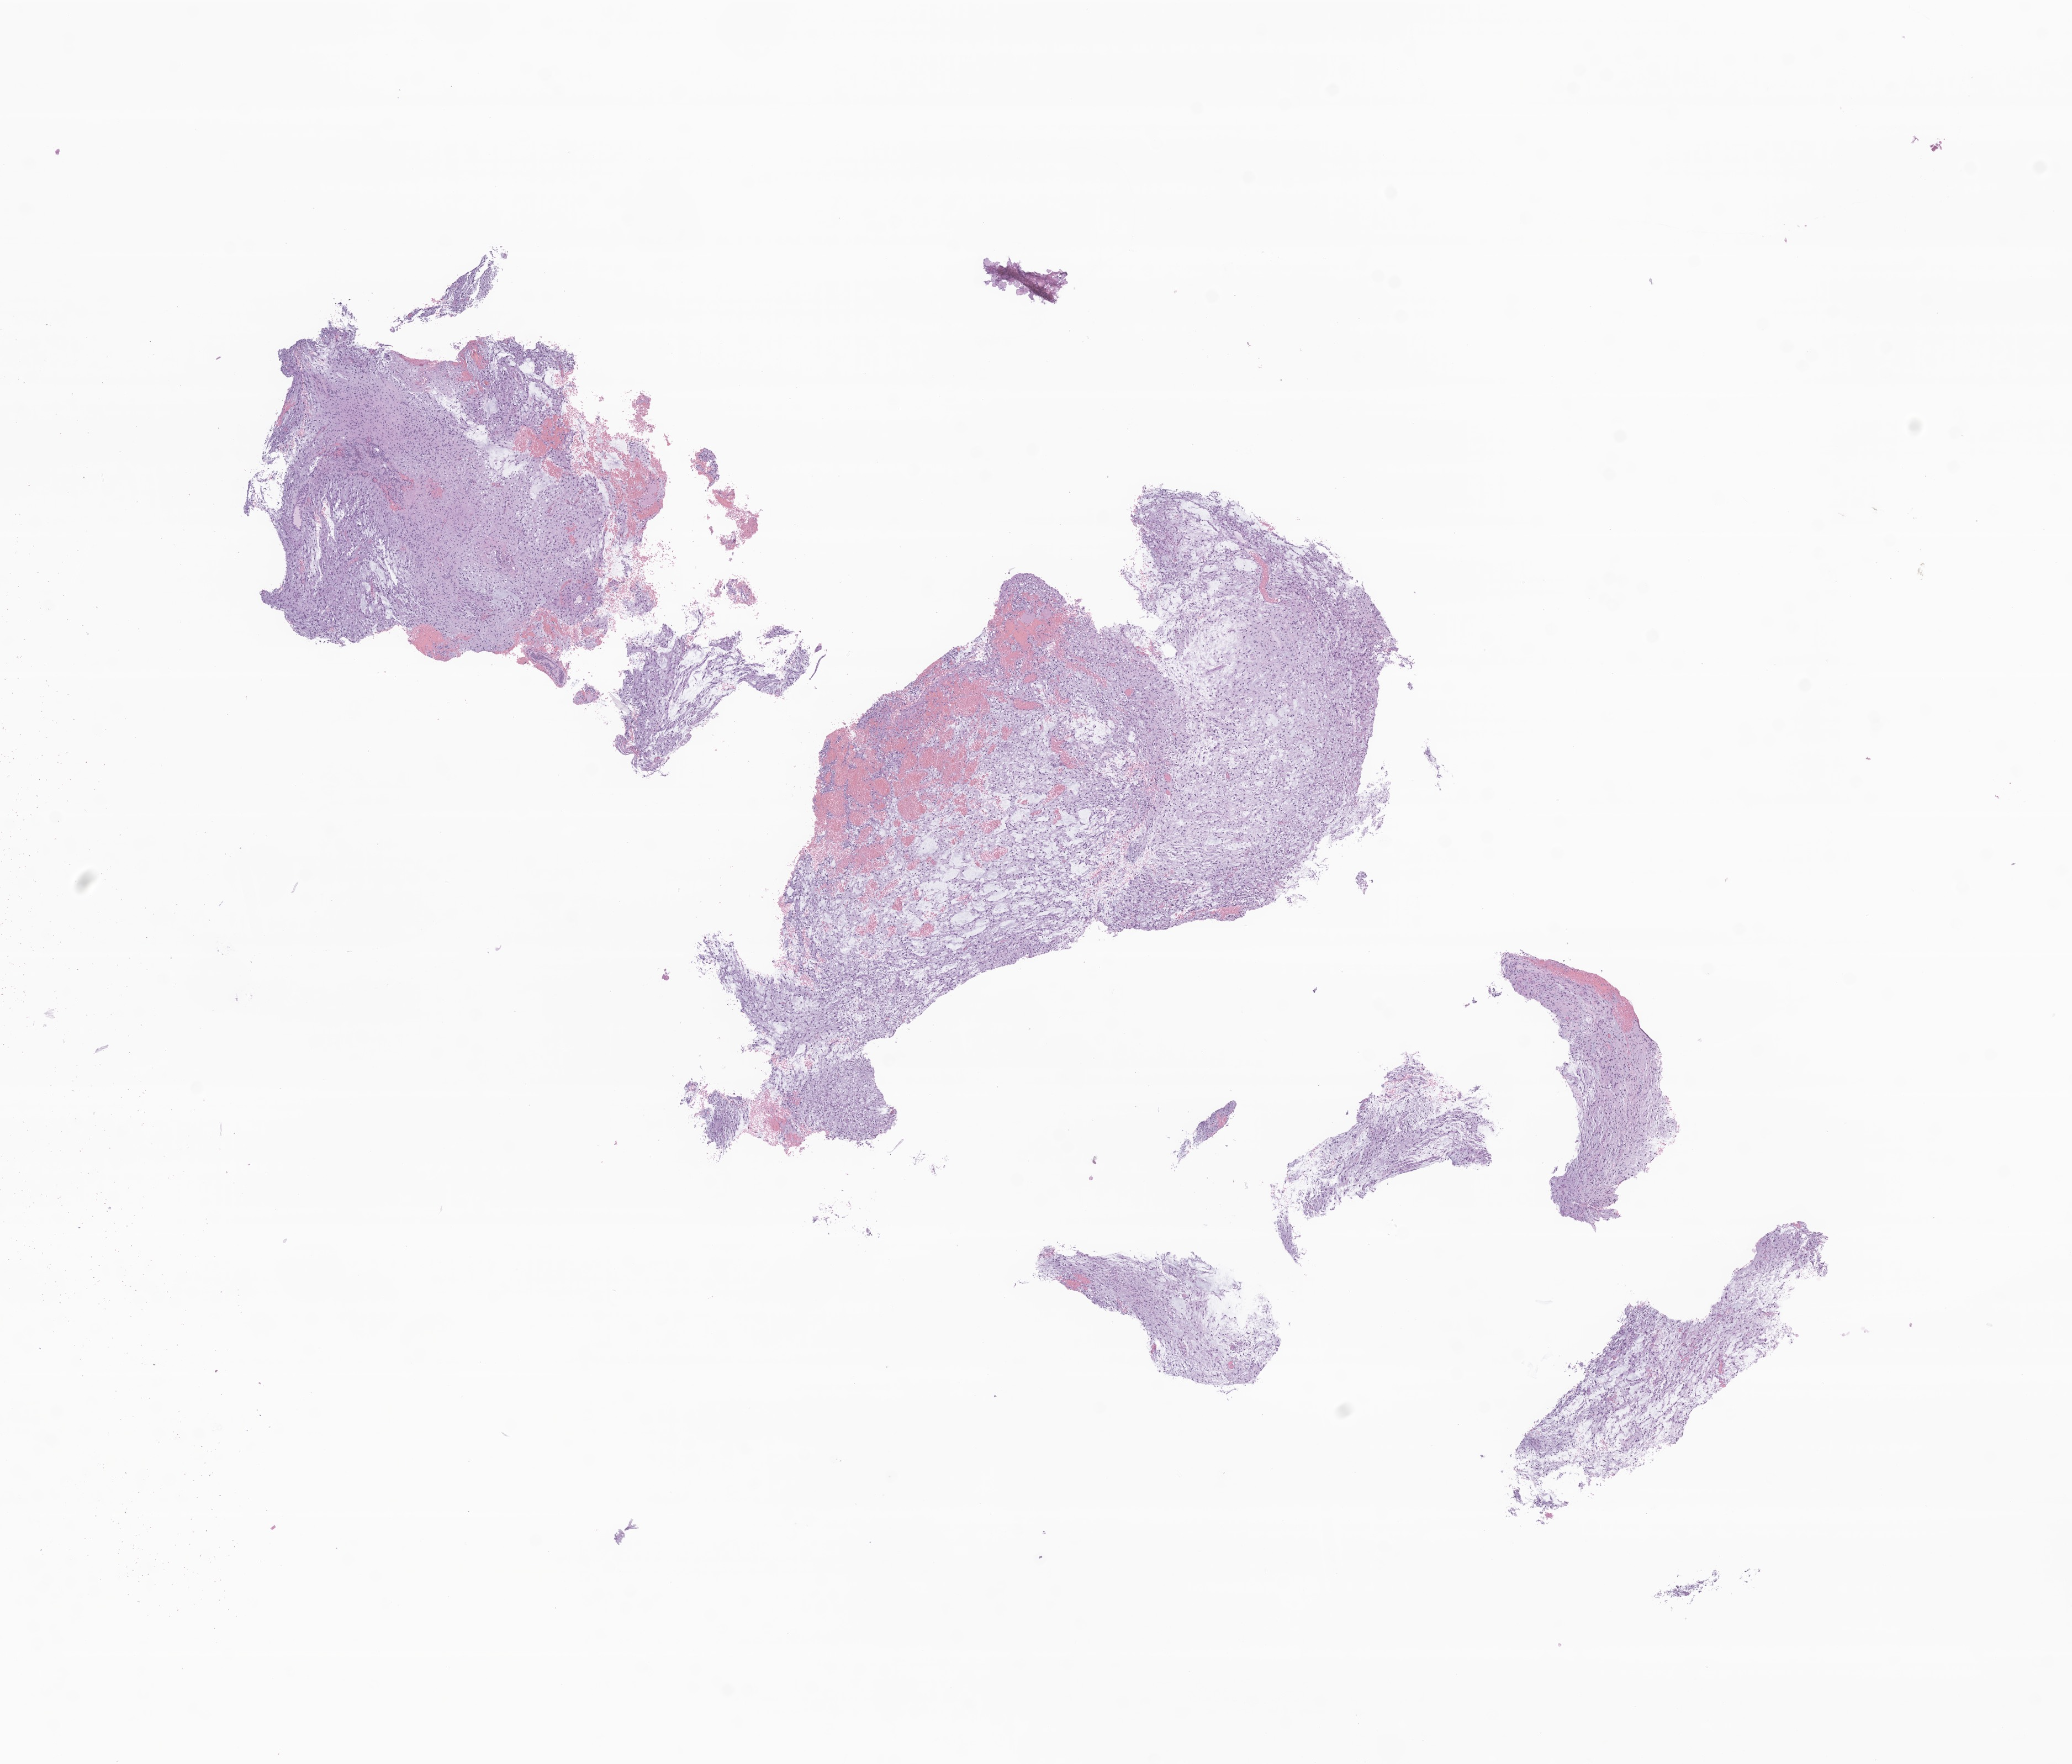
Digitized hematoxylin and eosin (H&E)-stained section of tumor tissue from the cerebellum — whole scanned area (about 15.8 x 13.5 mm) shown as a low-resolution overview, FFPE section. Patient: female, age 107 months (8 years 11 months).
Diagnosis (ICD-O-3 morphology term): Neoplasm, uncertain whether benign or malignant.